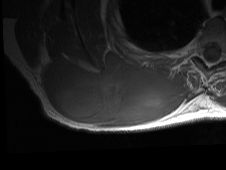
MRI of an extremity soft-tissue mass, one axial slice. Slice 31 of 81 in the series (ordered by position). MR volume resampled by the dataset authors to the PET/CT grid (not the native acquisition matrix). 3.27 mm slice thickness. 226 × 170 image matrix, field of view 221 × 166 mm. Male patient. From the clinical record (not read from this slice): histological type: pleiomorphic spindle cell undifferentiated; grade: high; site of the primary tumour: right parascapusular.
Outlined on this slice (expert contour drawn on MRI and transferred to this co-registered scan by the dataset authors):
- gross tumour volume including surrounding oedema: bounding box <42,52,191,128> (left, top, right, bottom; pixels)
- gross tumour volume (mass): <42,52,173,125>